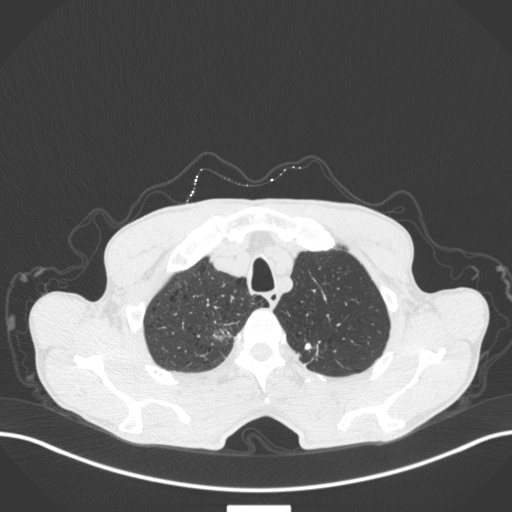
Chest CT, one axial slice; slice 374 of 445 in the series (ordered by position); 120 kVp; lung window (W 1500 / L -600 HU); 1 mm slice thickness; 512 × 512 image matrix, field of view 400 × 400 mm. Patient: male, 70 years. Case-level facts recorded for this patient, not image findings: clinical TNM (as recorded): T1a N0 M0; histopathological grade: G1-2.
Outlined on this slice (bounding box drawn by a radiologist):
- lung tumour (recorded histology: adenocarcinoma): bounding box (x1, y1, x2, y2) in pixels: (209, 322, 240, 344)